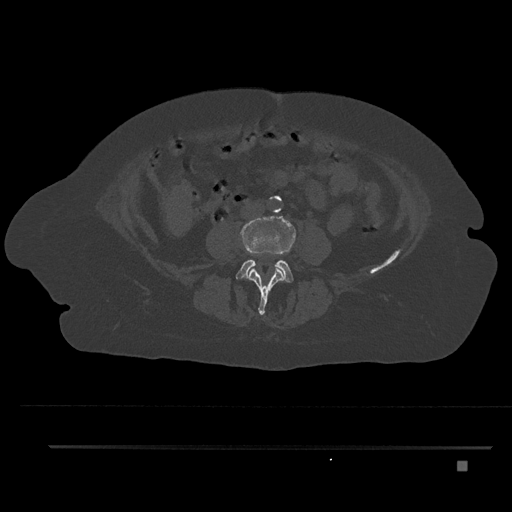
CT including the spine, one axial slice. Bone window (W 1800 / L 400 HU). 0.5 mm slice thickness. 512 × 512 image matrix, field of view 437 × 437 mm. Patient: female, 76 years. Case-level facts recorded for this patient, not image findings: primary cancer: lung; vertebrae with lytic lesions (as recorded): T11, L3.
Outlined on this slice (semi-automatic segmentation, software-assisted and operator-edited):
- L3 vertebra: bounding box [x1, y1, x2, y2] px = [249, 217, 288, 315]
- L4 vertebra: [235, 216, 296, 283]